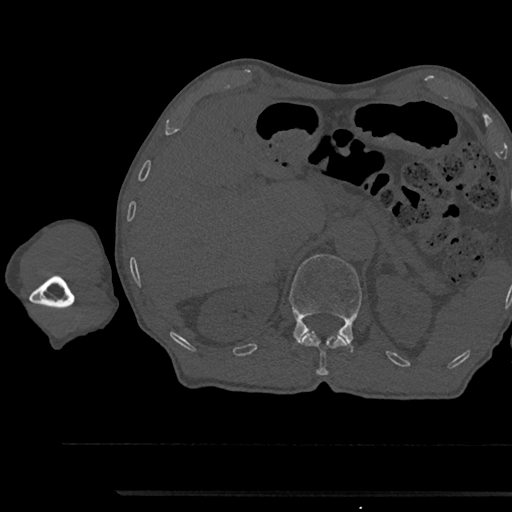
CT including the spine, one axial slice; position 673 of 797 along the scan axis; 120 kVp; bone window (W 1800 / L 400 HU); 0.5 mm slice thickness; 512 × 512 image matrix. Patient: male, 79 years. From the clinical record (not read from this slice): primary cancer: prostate.
Annotated regions visible in this slice (semi-automatically segmented with operator editing):
- L1 vertebra: bounding box (x1, y1, x2, y2) in pixels: (289, 254, 362, 353)
- T12 vertebra: (237, 331, 351, 375)